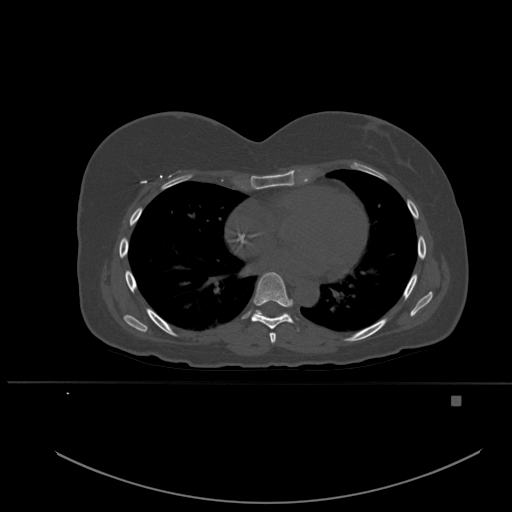
CT including the spine, one axial slice. Position 334 of 651 along the scan axis. Bone window (W 1800 / L 400 HU). 1.5 mm slice thickness. 512 × 512 image matrix. Patient: female, 49 years. From the clinical record (not read from this slice): primary cancer: breast; vertebrae with lytic lesions (as recorded): L3, T12, L4.
Outlined on this slice (semi-automatically segmented with operator editing):
- T6 vertebra: bounding box [x1, y1, x2, y2] px = [270, 333, 276, 343]
- T7 vertebra: [251, 272, 294, 329]
- T8 vertebra: [256, 310, 286, 316]